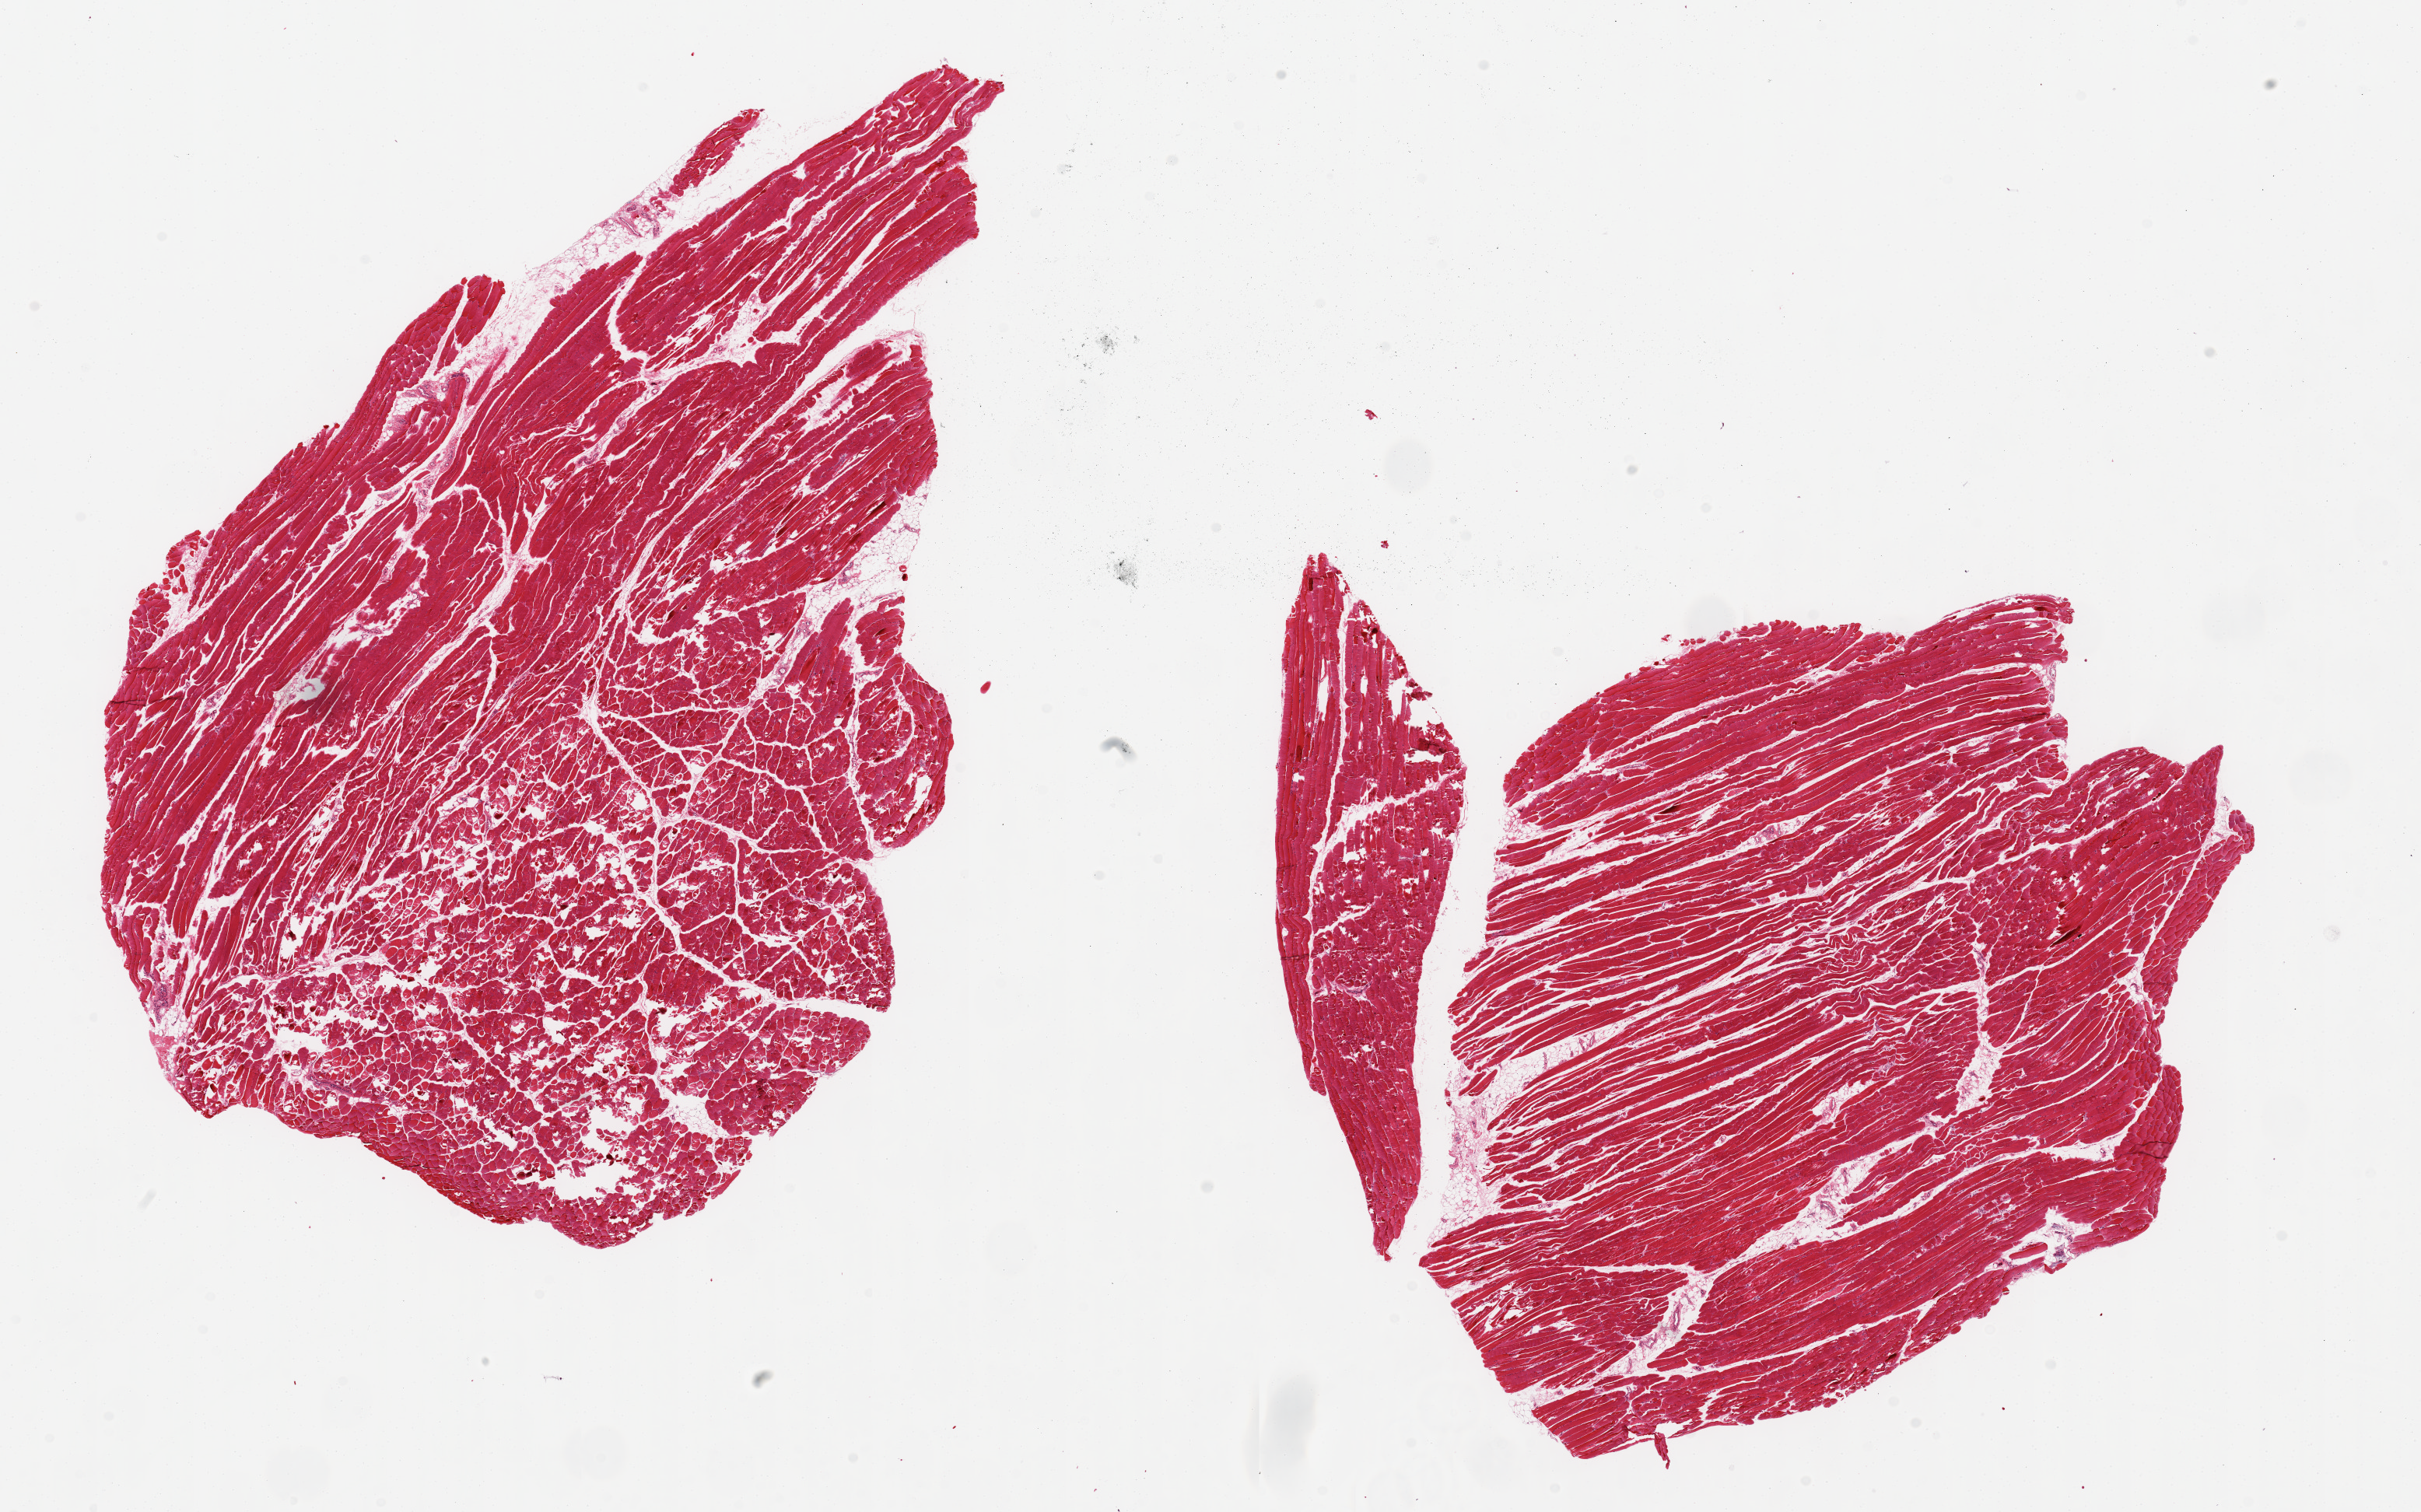
H&E whole-slide image, brightfield — a low-resolution overview of the entire scanned area, about 24.6 x 15.4 mm. PAXgene-fixed paraffin-embedded (PFPE) section. Sampled site (target tissue): skeletal muscle. Tissue donor sample. Donor: female.
Reviewer comment on this tissue sample: 2 aliquots, ~10x7mm, minimal interstitial fat.